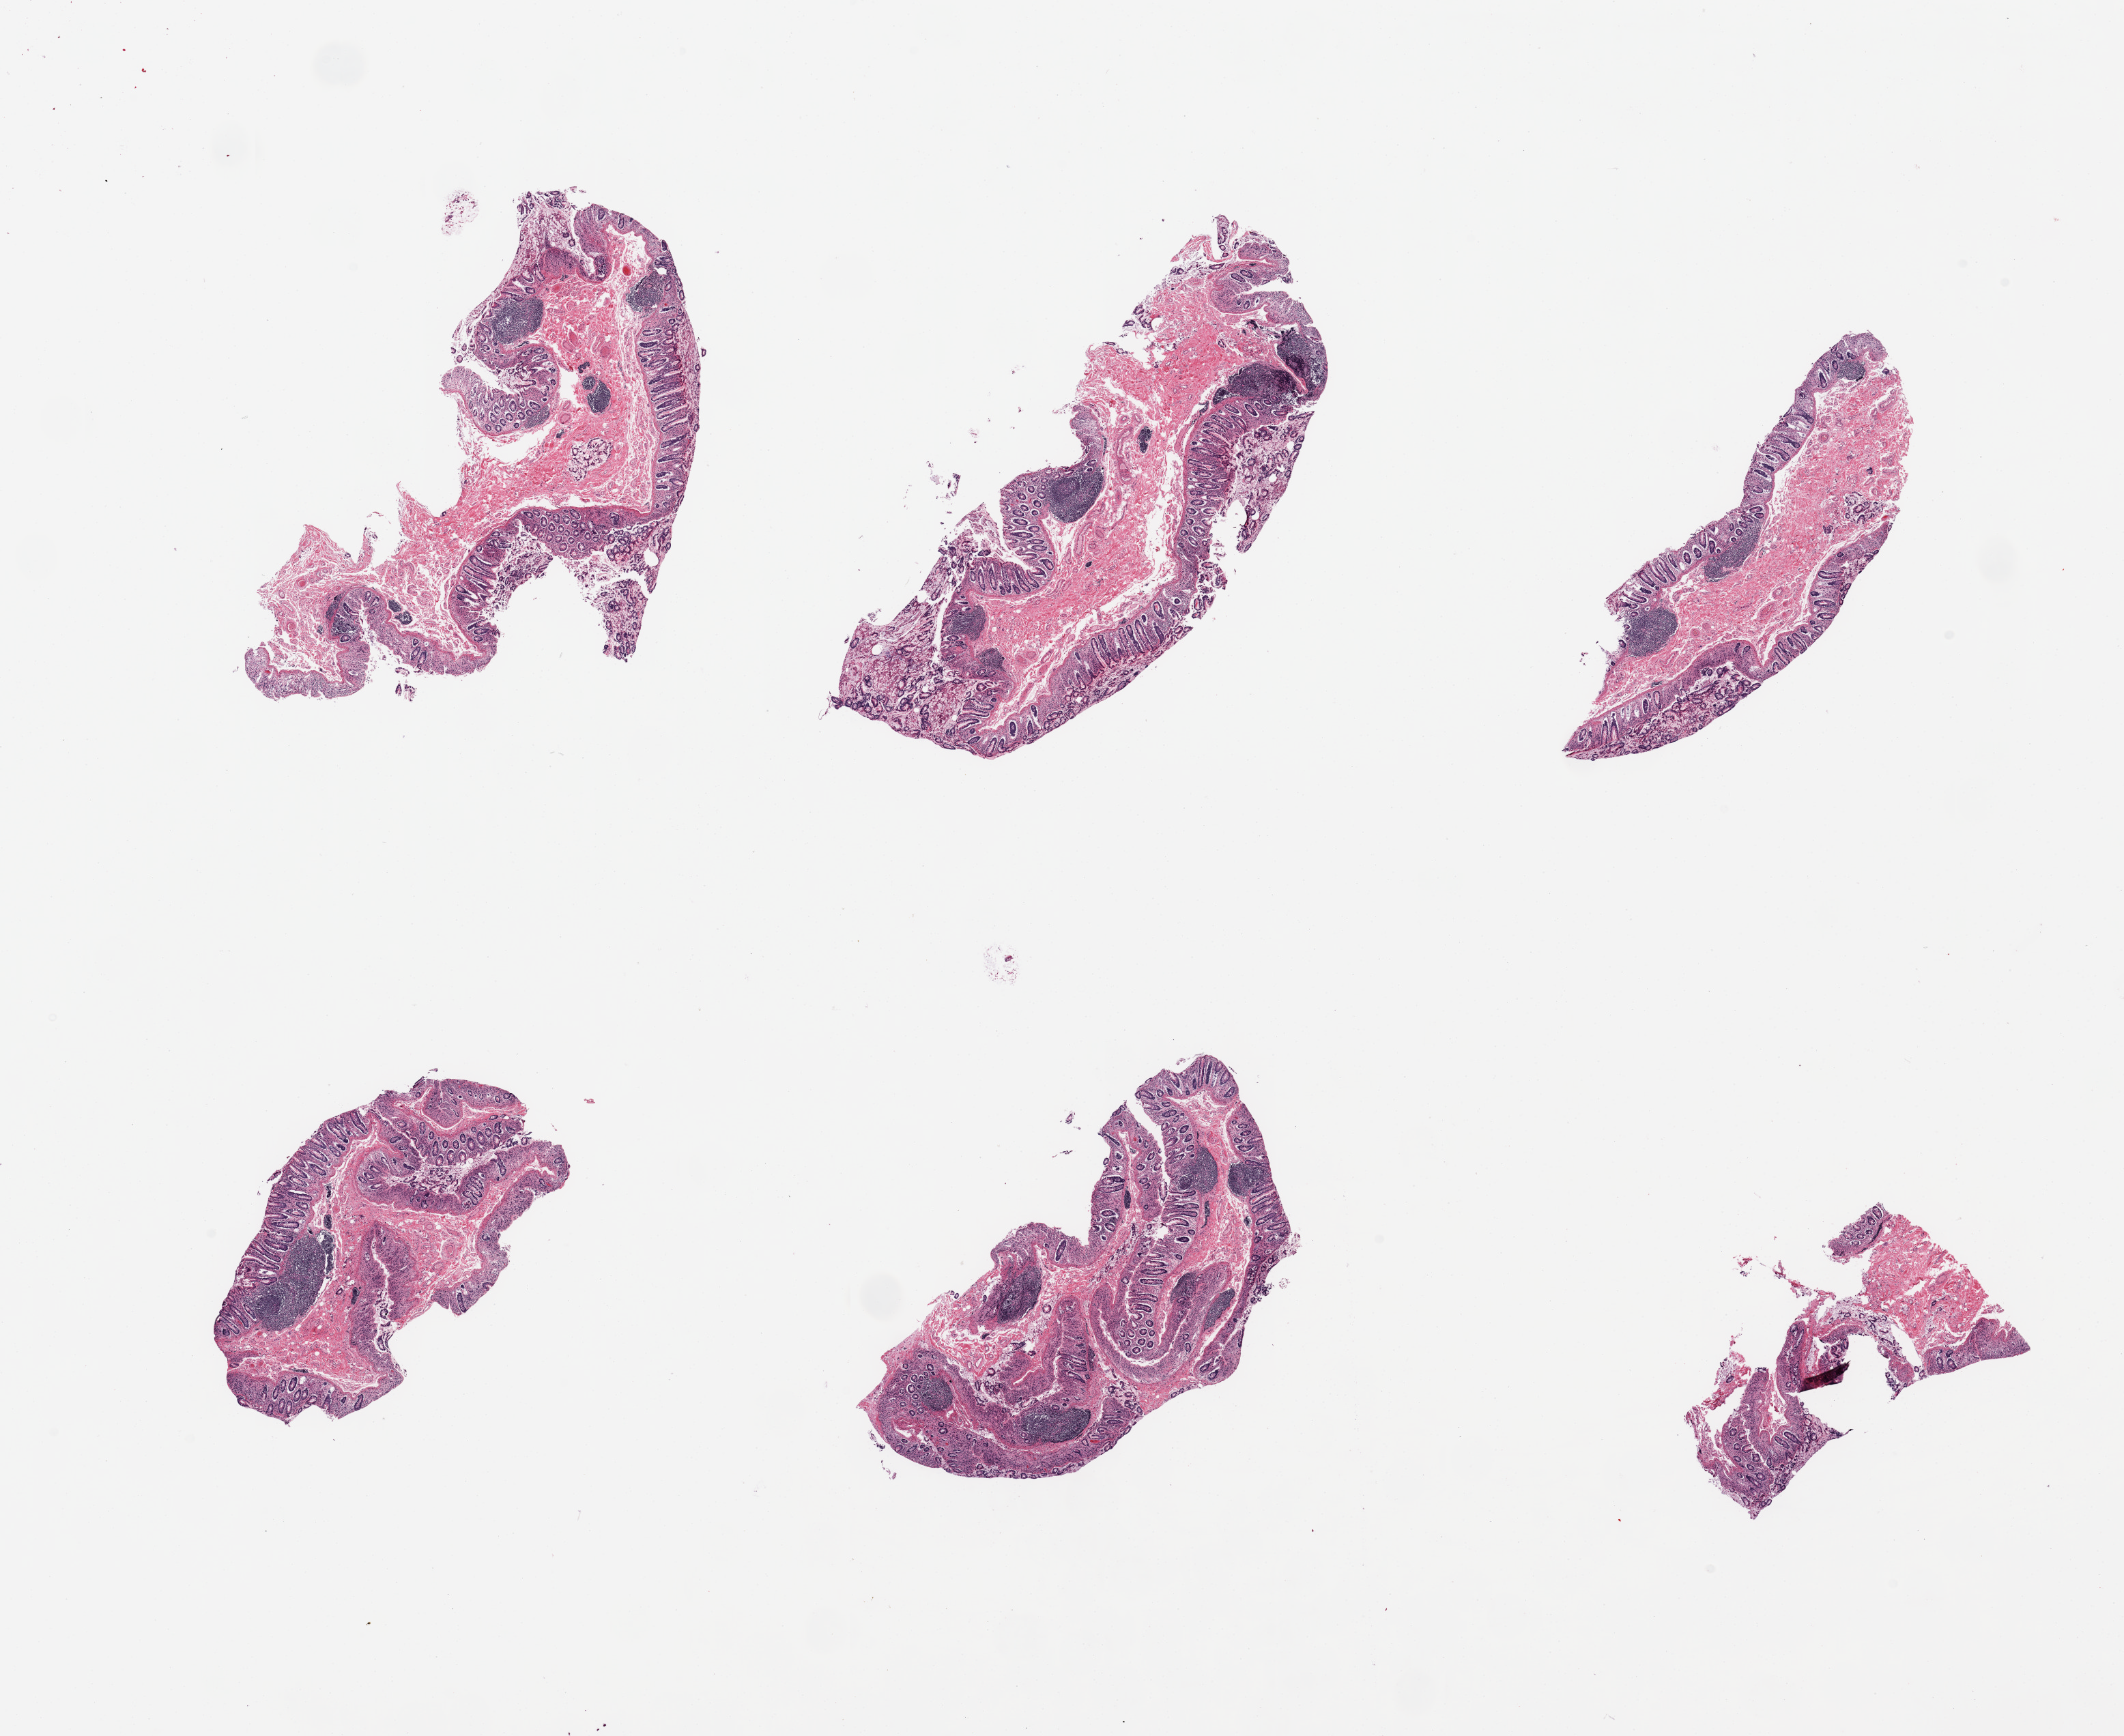
H&E whole-slide image, brightfield — low-resolution overview of the scanned area, about 24.6 x 20.1 mm. PAXgene-fixed, paraffin-embedded tissue. Section of ileum (target tissue). Donor tissue sample. Donor: female.
Reviewer comment on this tissue sample: 6 pieces, target lymphoid aggregates ~20% total tissue.